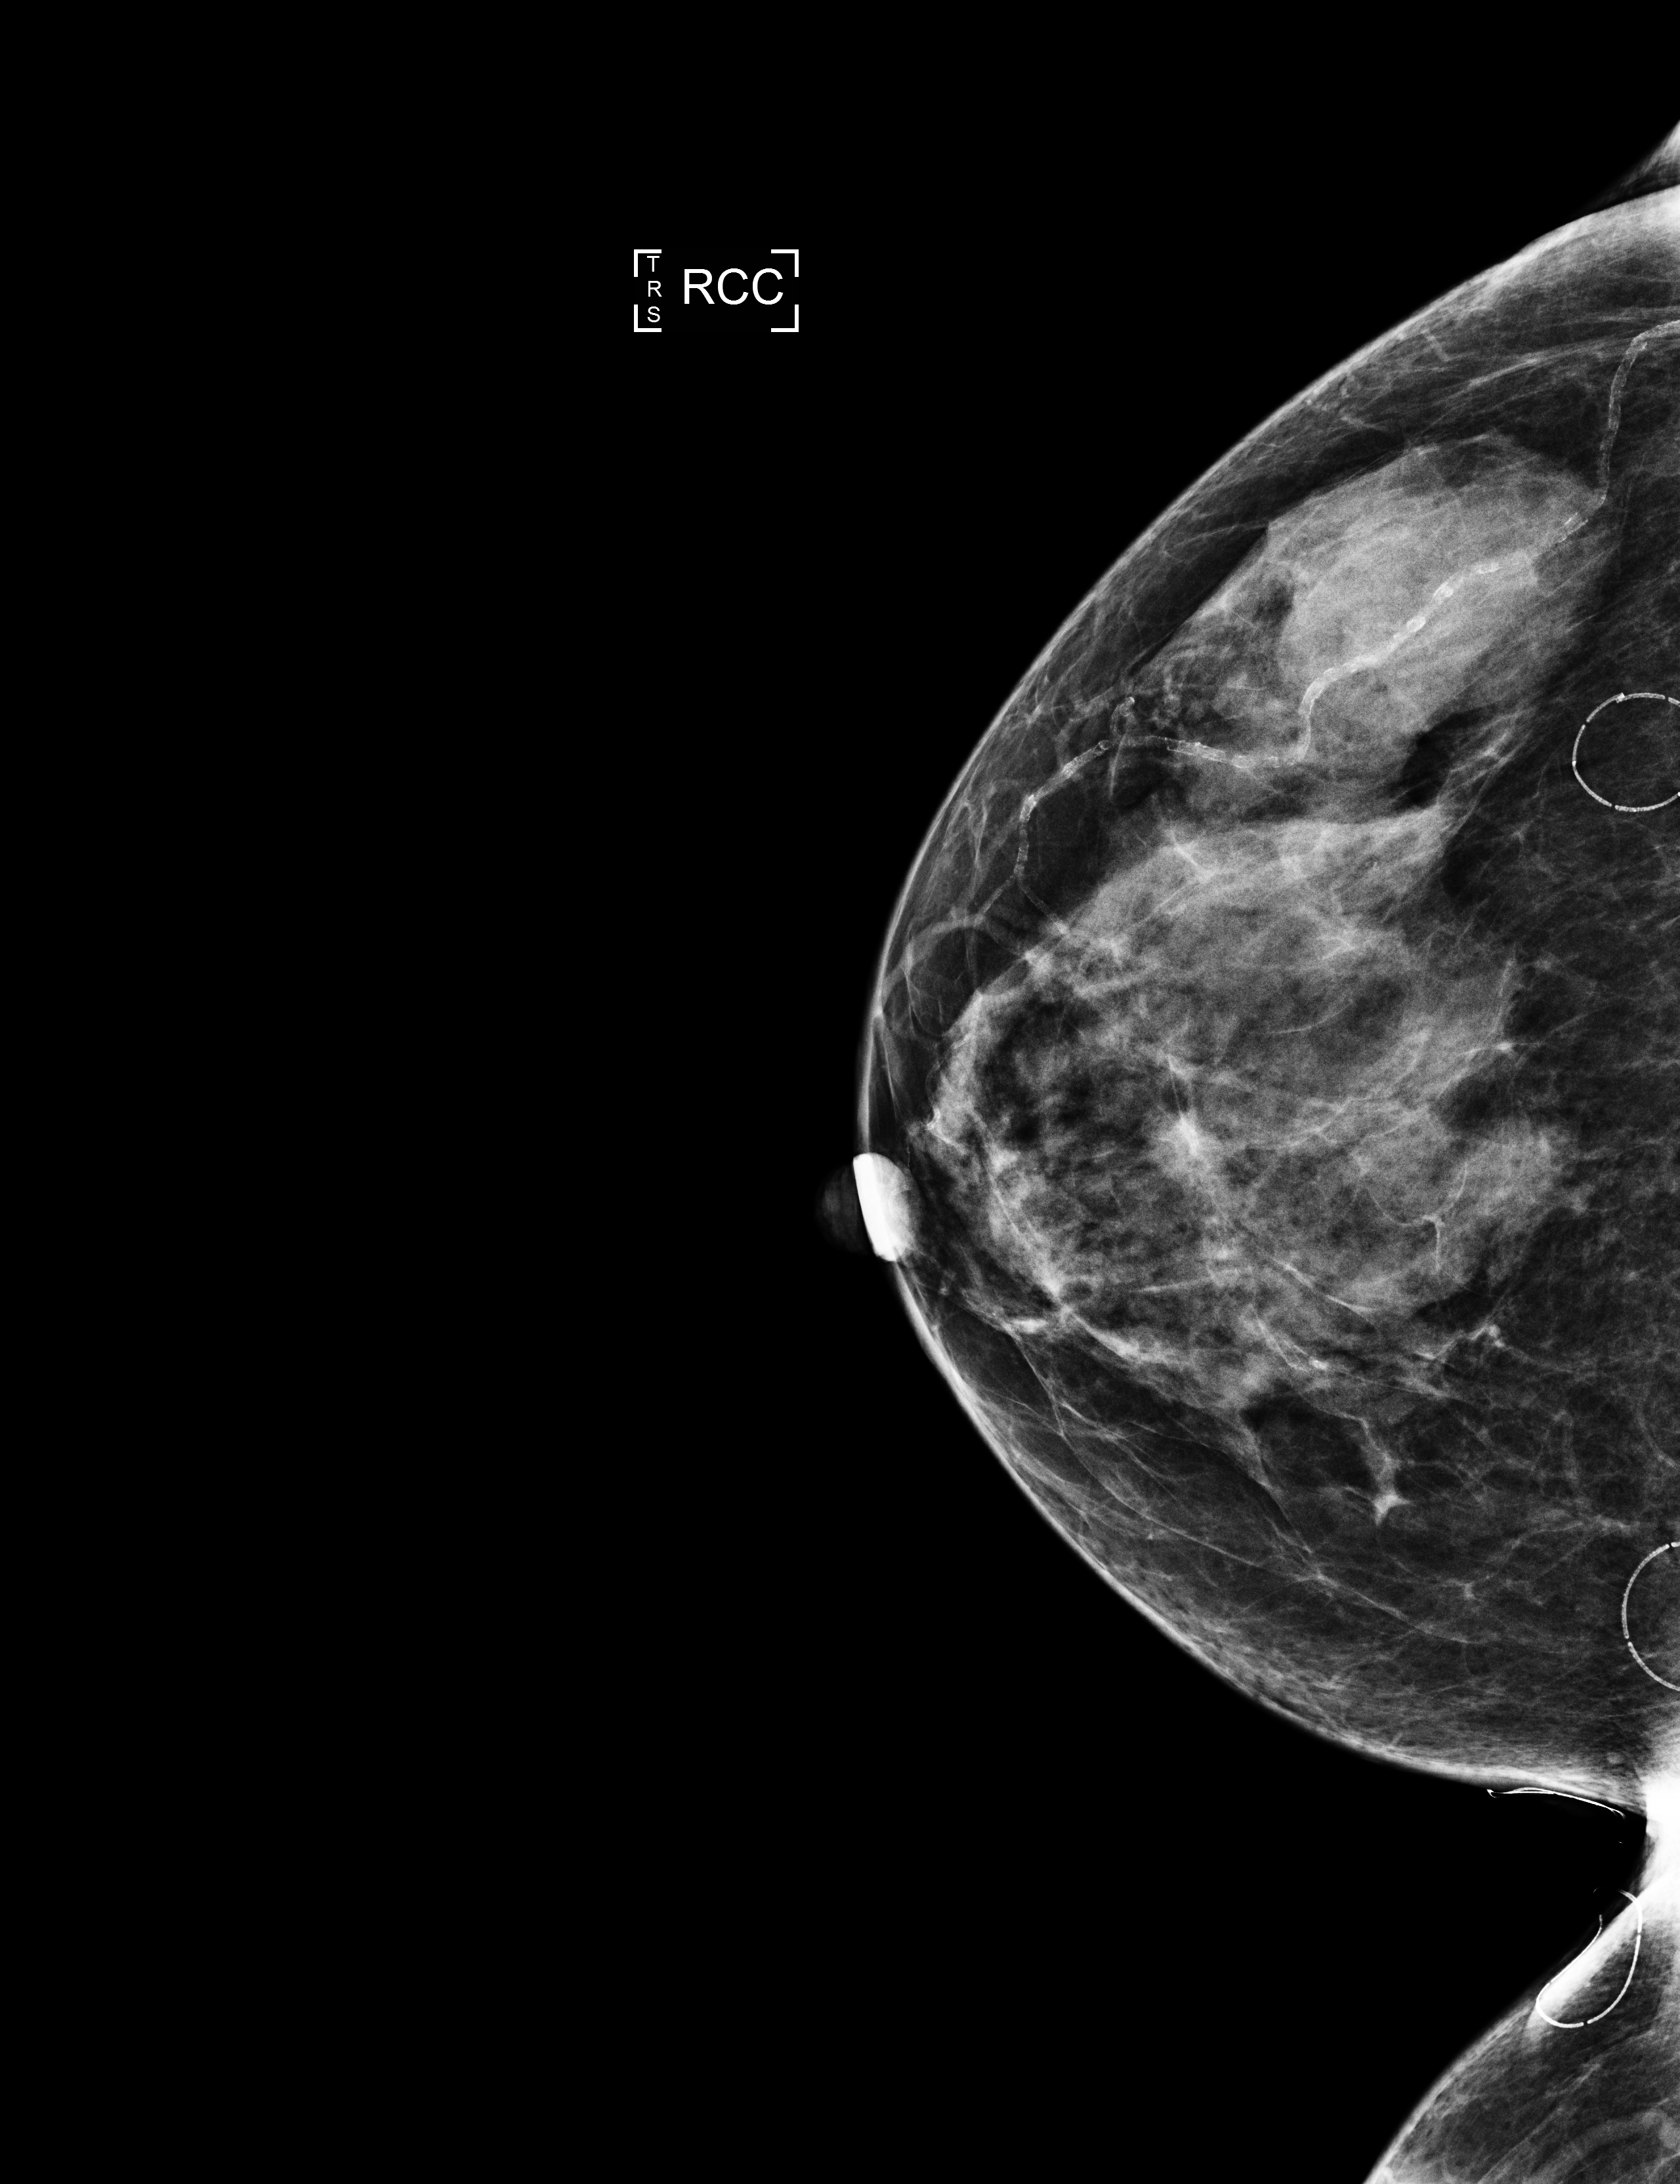
Digital mammogram (FFDM), right breast, craniocaudal (CC) view, screening examination, system: Selenia Dimensions. Female patient, age 75 years.
Breast density at the screening exam (both breasts): heterogeneously dense (BI-RADS density category c). Final BI-RADS category for the screening round (tomosynthesis exam, both breasts): category 1. Recall: no recall after this screen.